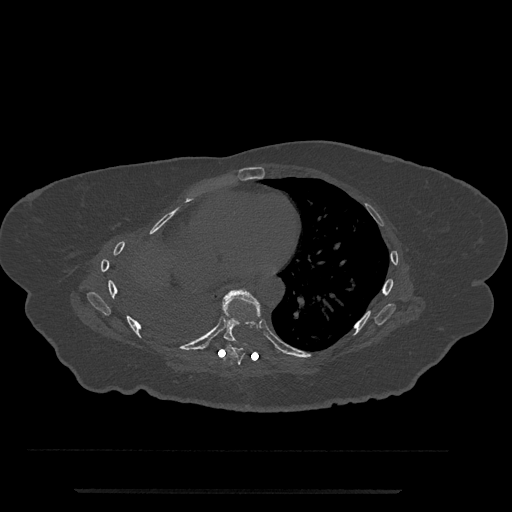
CT including the spine, one axial slice; slice 417 of 797 in the series (ordered by position); reconstruction kernel Br40s/3; bone window (W 1800 / L 400 HU); 0.5 mm slice thickness; 512 × 512 image matrix, field of view 440 × 440 mm. Patient: female, 51 years. Case-level facts recorded for this patient, not image findings: primary cancer: neuro.
Outlined on this slice (semi-automatic segmentation, software-assisted and operator-edited):
- T7 vertebra: box from (x=224, y=345) to (x=245, y=365) px
- T8 vertebra: (x=222, y=288)–(x=261, y=342)